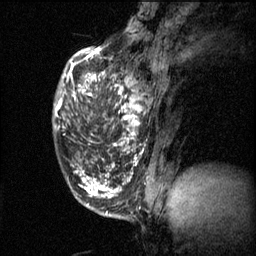
Breast MRI (dynamic contrast-enhanced), one sagittal slice; slice 17 of 60 in the series (ordered by position); 3 images stored at this slice position (order not interpretable as contrast timing); 1.5 T; TE 4.2 ms, TR 11.1 ms; 2 mm slice thickness; 256 × 256 image matrix, field of view 180 × 180 mm. Female patient, age 50 years.
Structures marked on this image (semi-automatically segmented with operator editing):
- analysis volume of interest (the breast-tissue region the enhancement analysis was run in; not a lesion): bounding box (x1, y1, x2, y2) in pixels: (81, 68, 153, 141)
- tumour enhancement mask (voxels above the 70 % enhancement threshold inside the analysis volume of interest): (81, 70, 143, 141)